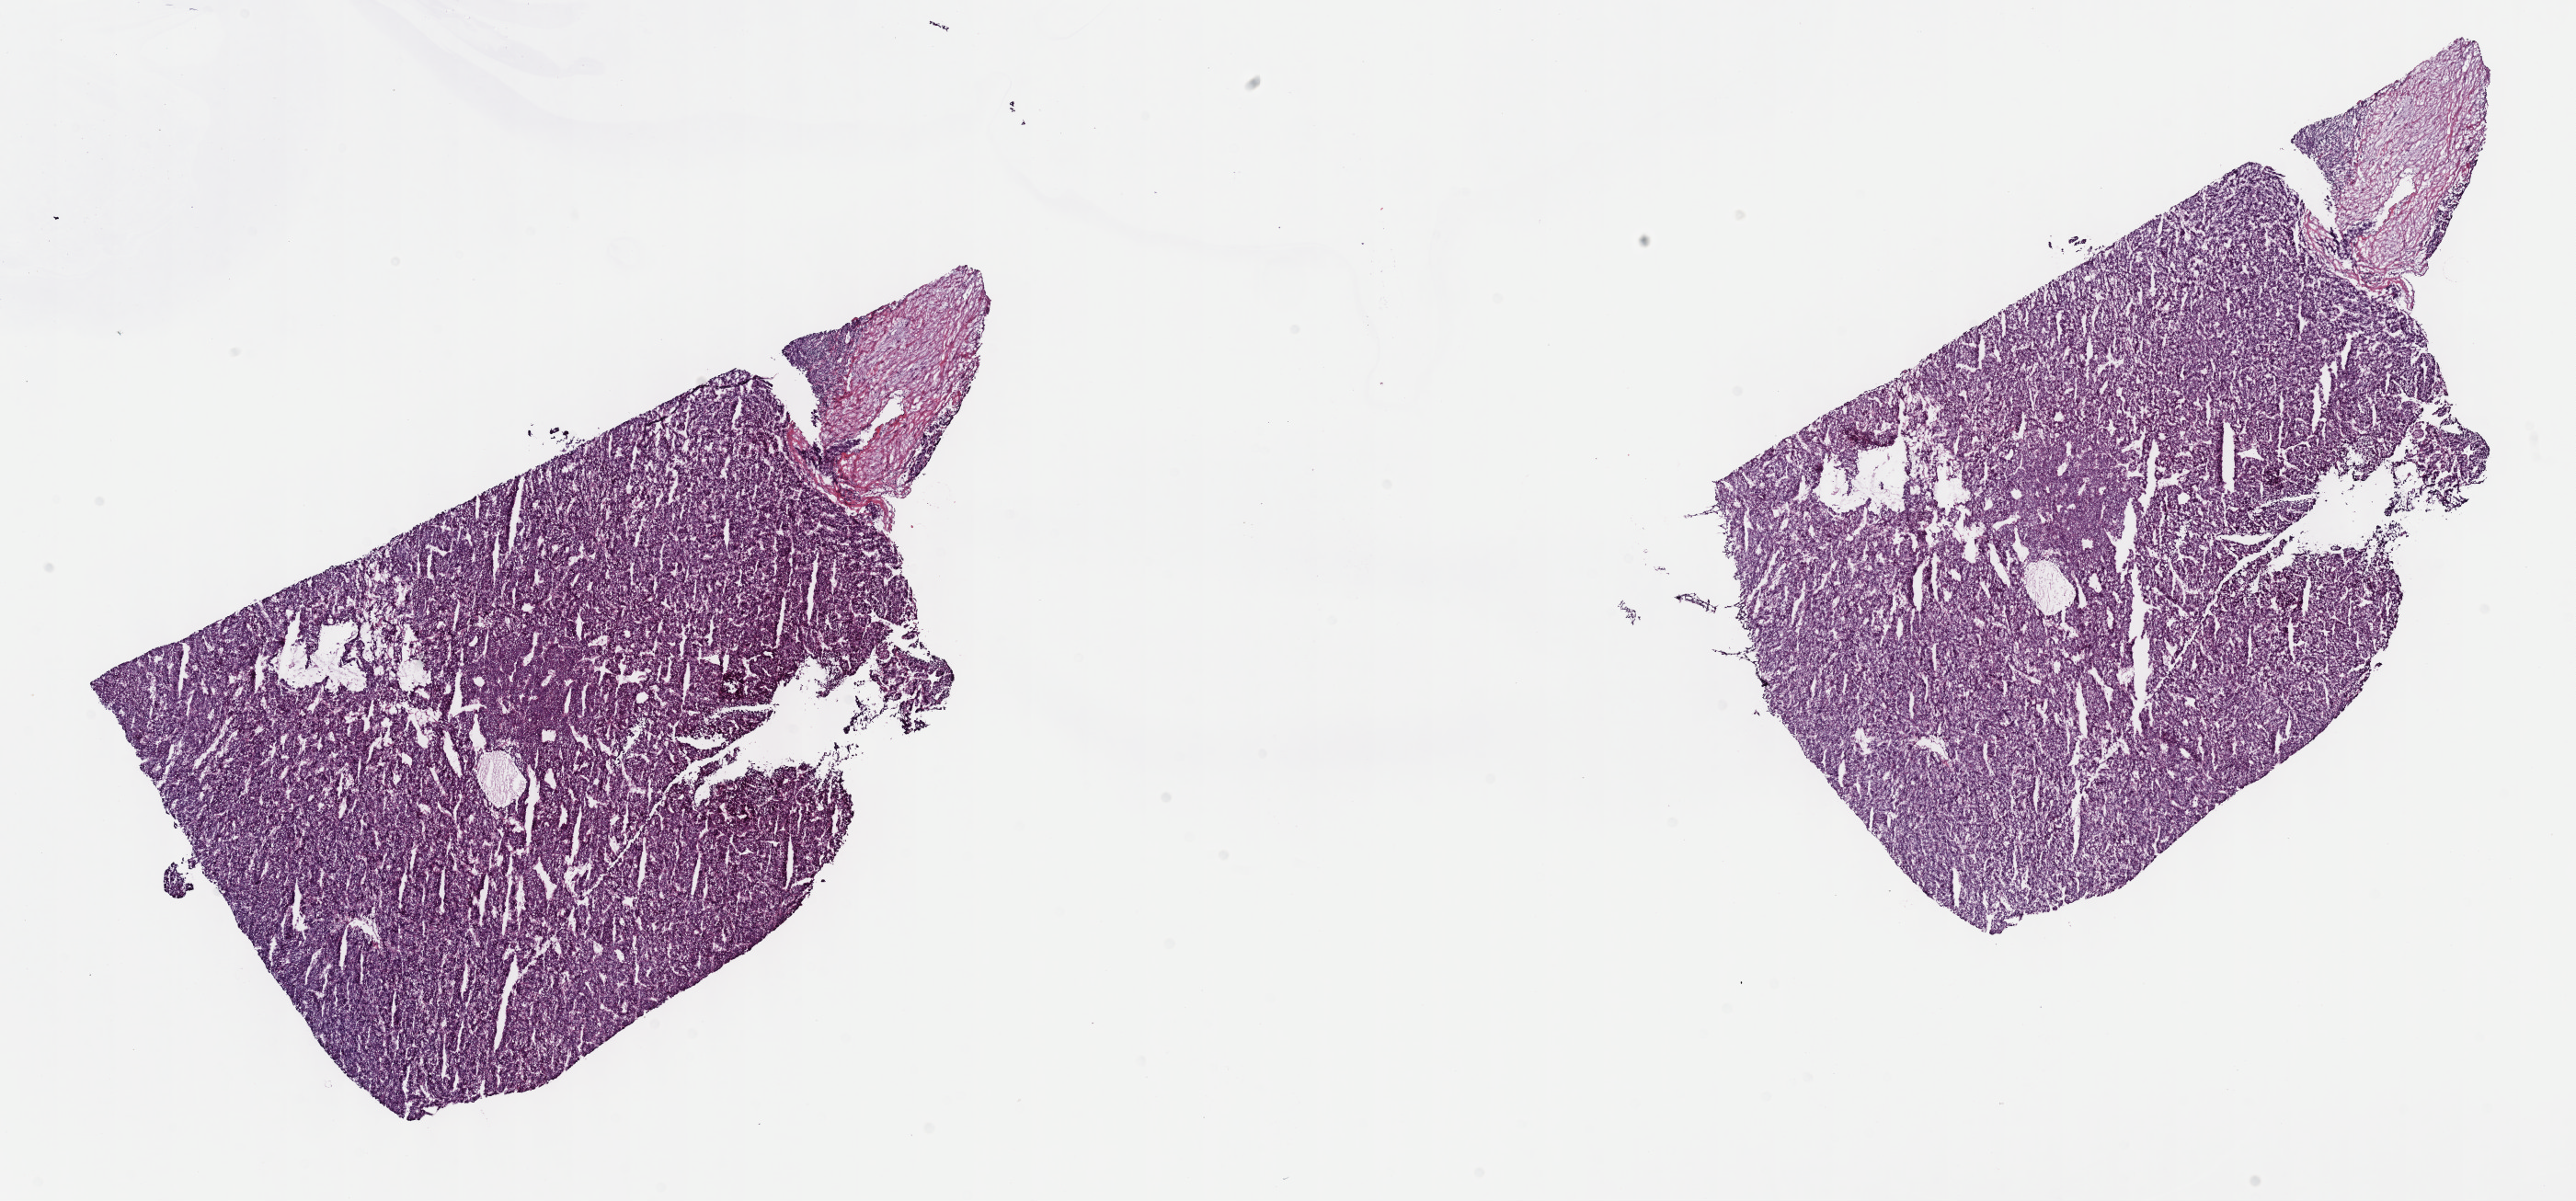
H&E whole-slide image, shown as a low-resolution overview of the whole scanned area (about 22.7 x 10.6 mm, slide scanned at 40x). Frozen section from the top of the tissue portion. Primary tumour sample from the liver. Male patient; age at initial diagnosis 52 years. Histologic grade: G4 (undifferentiated). Pathologist review of this section (percent, as recorded): tumour cells 85%, tumour nuclei 95%, normal cells 0%, stromal cells 15%, necrosis 0%. Inflammatory infiltration, as recorded: lymphocyte infiltration 0%, monocyte infiltration 0%, neutrophil infiltration 0%.
* diagnosis: Hepatocellular carcinoma, NOS
* AJCC pathologic stage: II (6th edition)